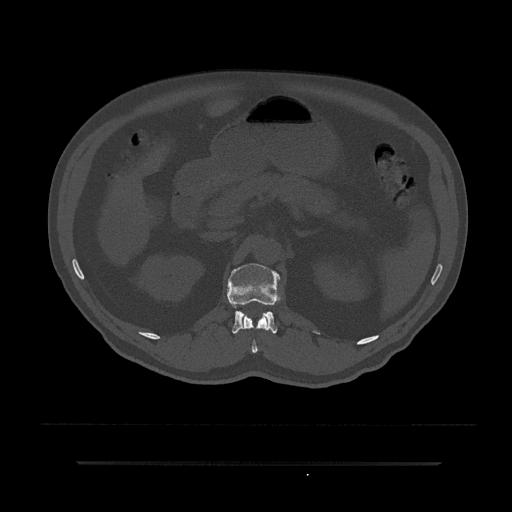
CT including the spine, one axial slice; bone window (W 1800 / L 400 HU); 0.5 mm slice thickness; 512 × 512 image matrix, field of view 464 × 464 mm. Male patient, age 59 years. Case-level facts recorded for this patient, not image findings: primary cancer: bile ducts.
Structures marked on this image (semi-automatic segmentation, software-assisted and operator-edited):
- L1 vertebra: bounding box [x1, y1, x2, y2] px = [228, 263, 280, 334]
- T12 vertebra: [240, 315, 268, 354]